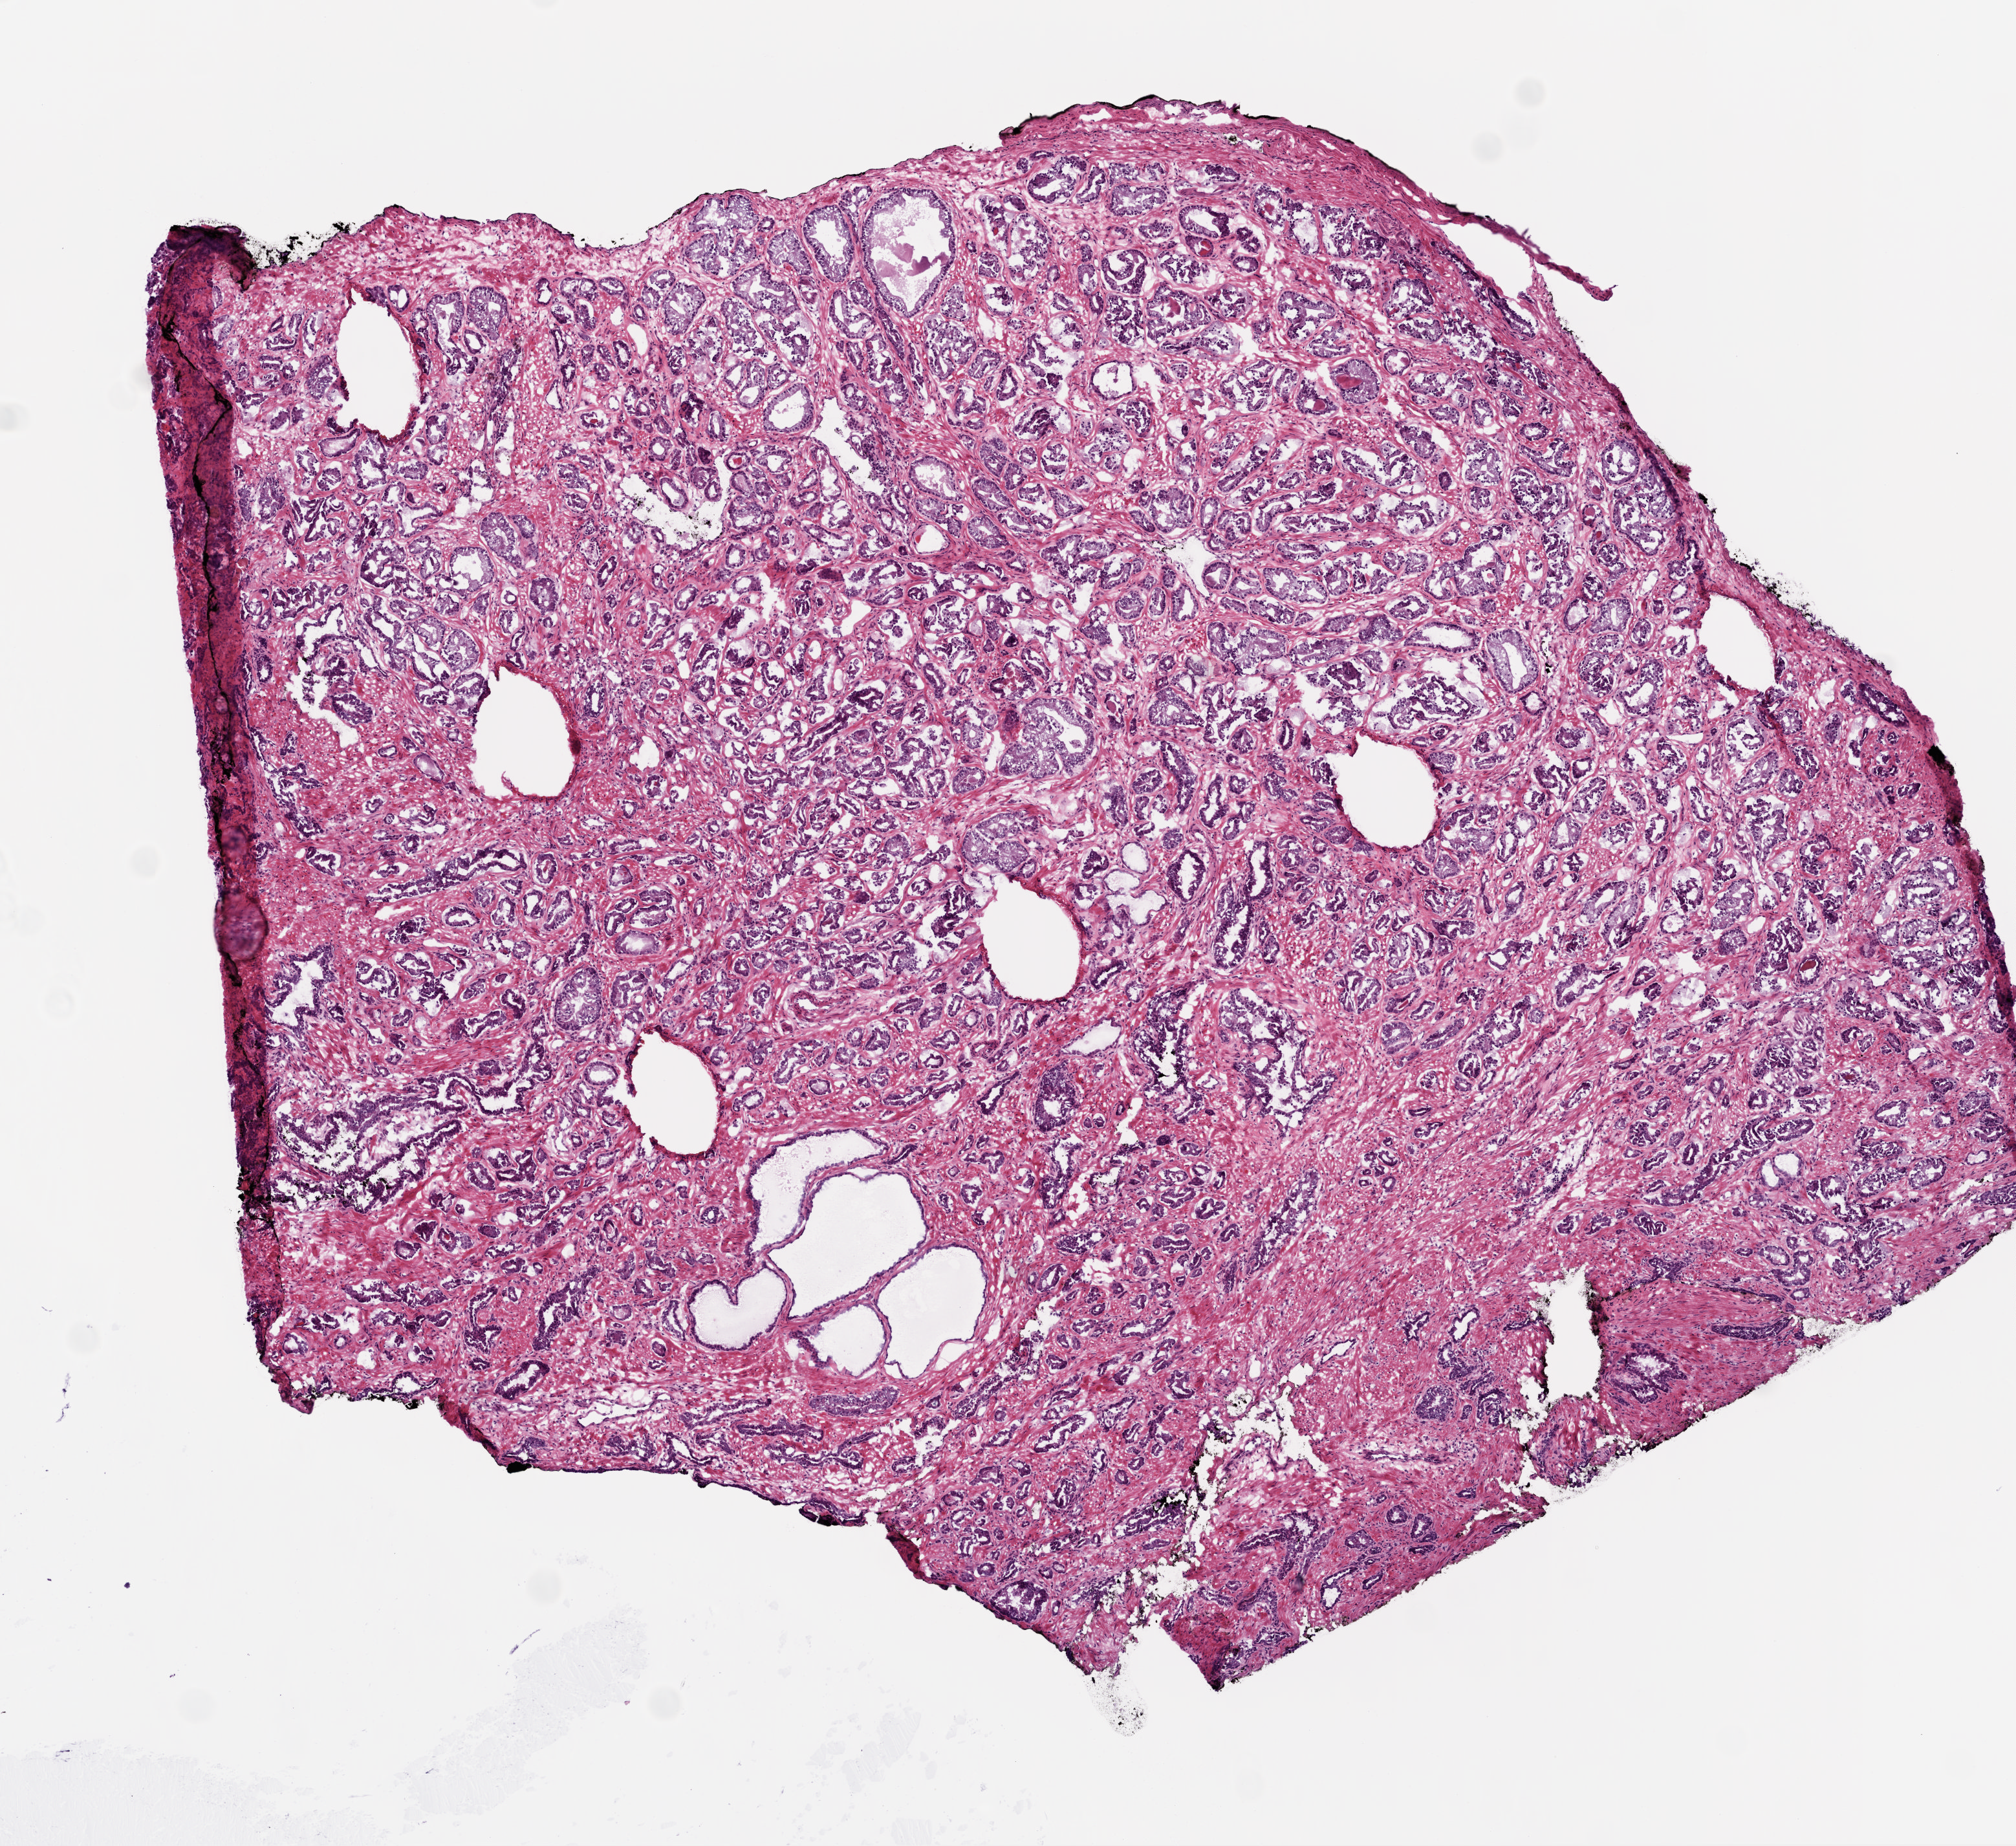
Whole-slide histology image, Hematoxylin and eosin (H&E) stained — whole scanned area (about 6.3 x 5.8 mm, from a 20x scan) shown as a low-resolution overview; frozen section; primary tumour sample from the prostate. Male patient; age at initial diagnosis 48 years. Gleason score: 6 (3+3). Composition of this section per pathologist review: tumour cells 85%, tumour nuclei 65%, normal cells 10%, stromal cells 5%, necrosis 0%.
Laterality: bilateral. Diagnosis: Acinar cell carcinoma (prostate gland).